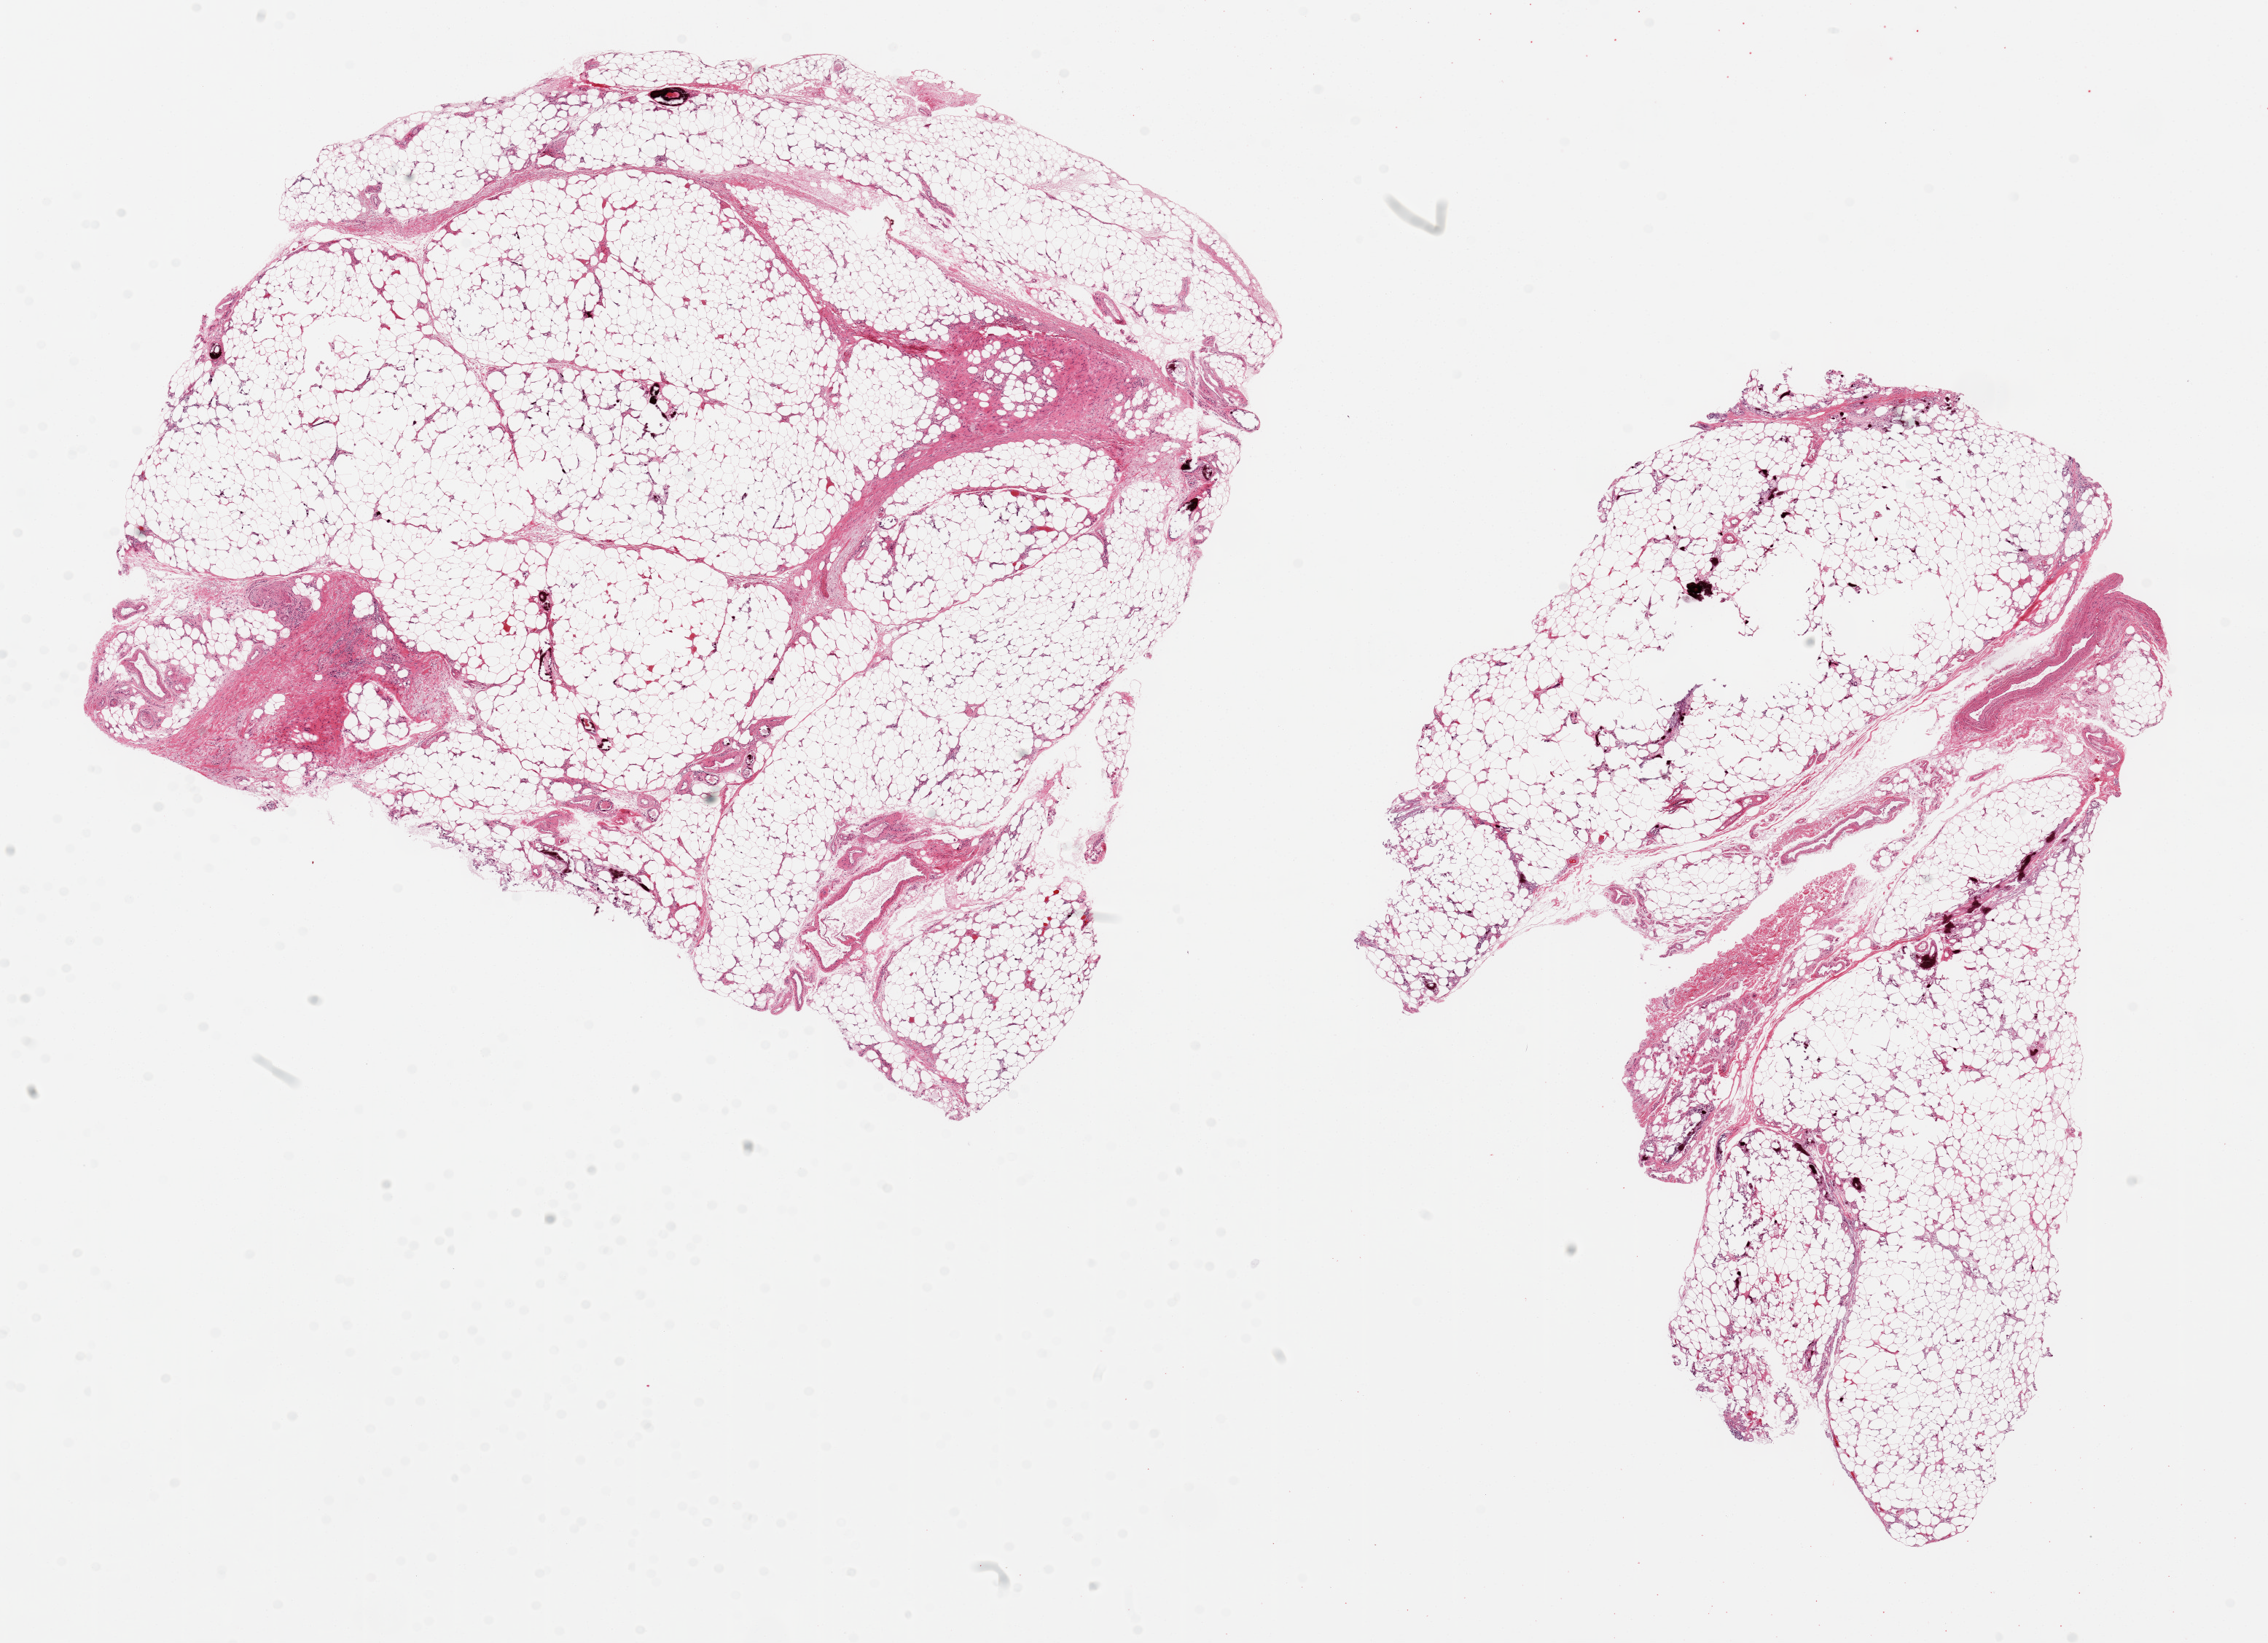
Whole-slide image, haematoxylin and eosin stain, brightfield, a low-resolution overview of the entire scanned area, about 24.6 x 17.8 mm; PAXgene-fixed paraffin-embedded (PFPE) section; sampled site (target tissue): adipose tissue; donor tissue sample. Donor sex: female.
Review note (as recorded): 2 ~ 11x8mm aliquots.